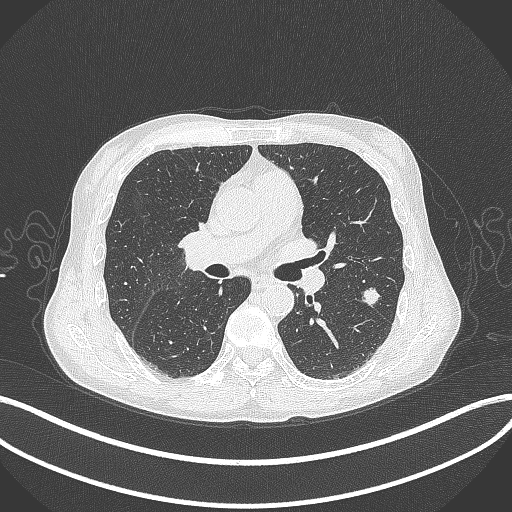
Chest CT, one axial slice. Slice 204 of 429 in the series (ordered by position). Reconstruction kernel B70f. Lung window (W 1500 / L -600 HU). 512 × 512 image matrix, field of view 400 × 400 mm. Male patient, age 58 years. From the clinical record (not read from this slice): clinical TNM (as recorded): T1c N0 M0; histopathological grade: G2.
Outlined on this slice (bounding box drawn by a radiologist):
- lung tumour (recorded histology: adenocarcinoma): bounding box <360,286,383,307> (left, top, right, bottom; pixels)